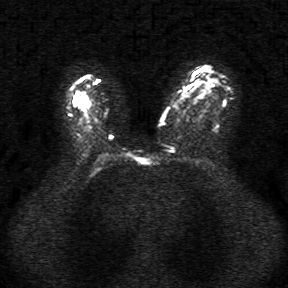
Breast MRI, one axial slice; slice 23 of 34 in the series (ordered by position); diffusion-weighted series; image 2 of 4 stored at this slice position (different b-values; order by instance number); 1.5 T; 5 mm slice thickness; 288 × 288 image matrix, field of view 340 × 340 mm. Female patient.
Annotated regions visible in this slice (manually delineated by an expert):
- tumour on diffusion-weighted imaging: bounding box (x1, y1, x2, y2) in pixels: (74, 98, 78, 104)